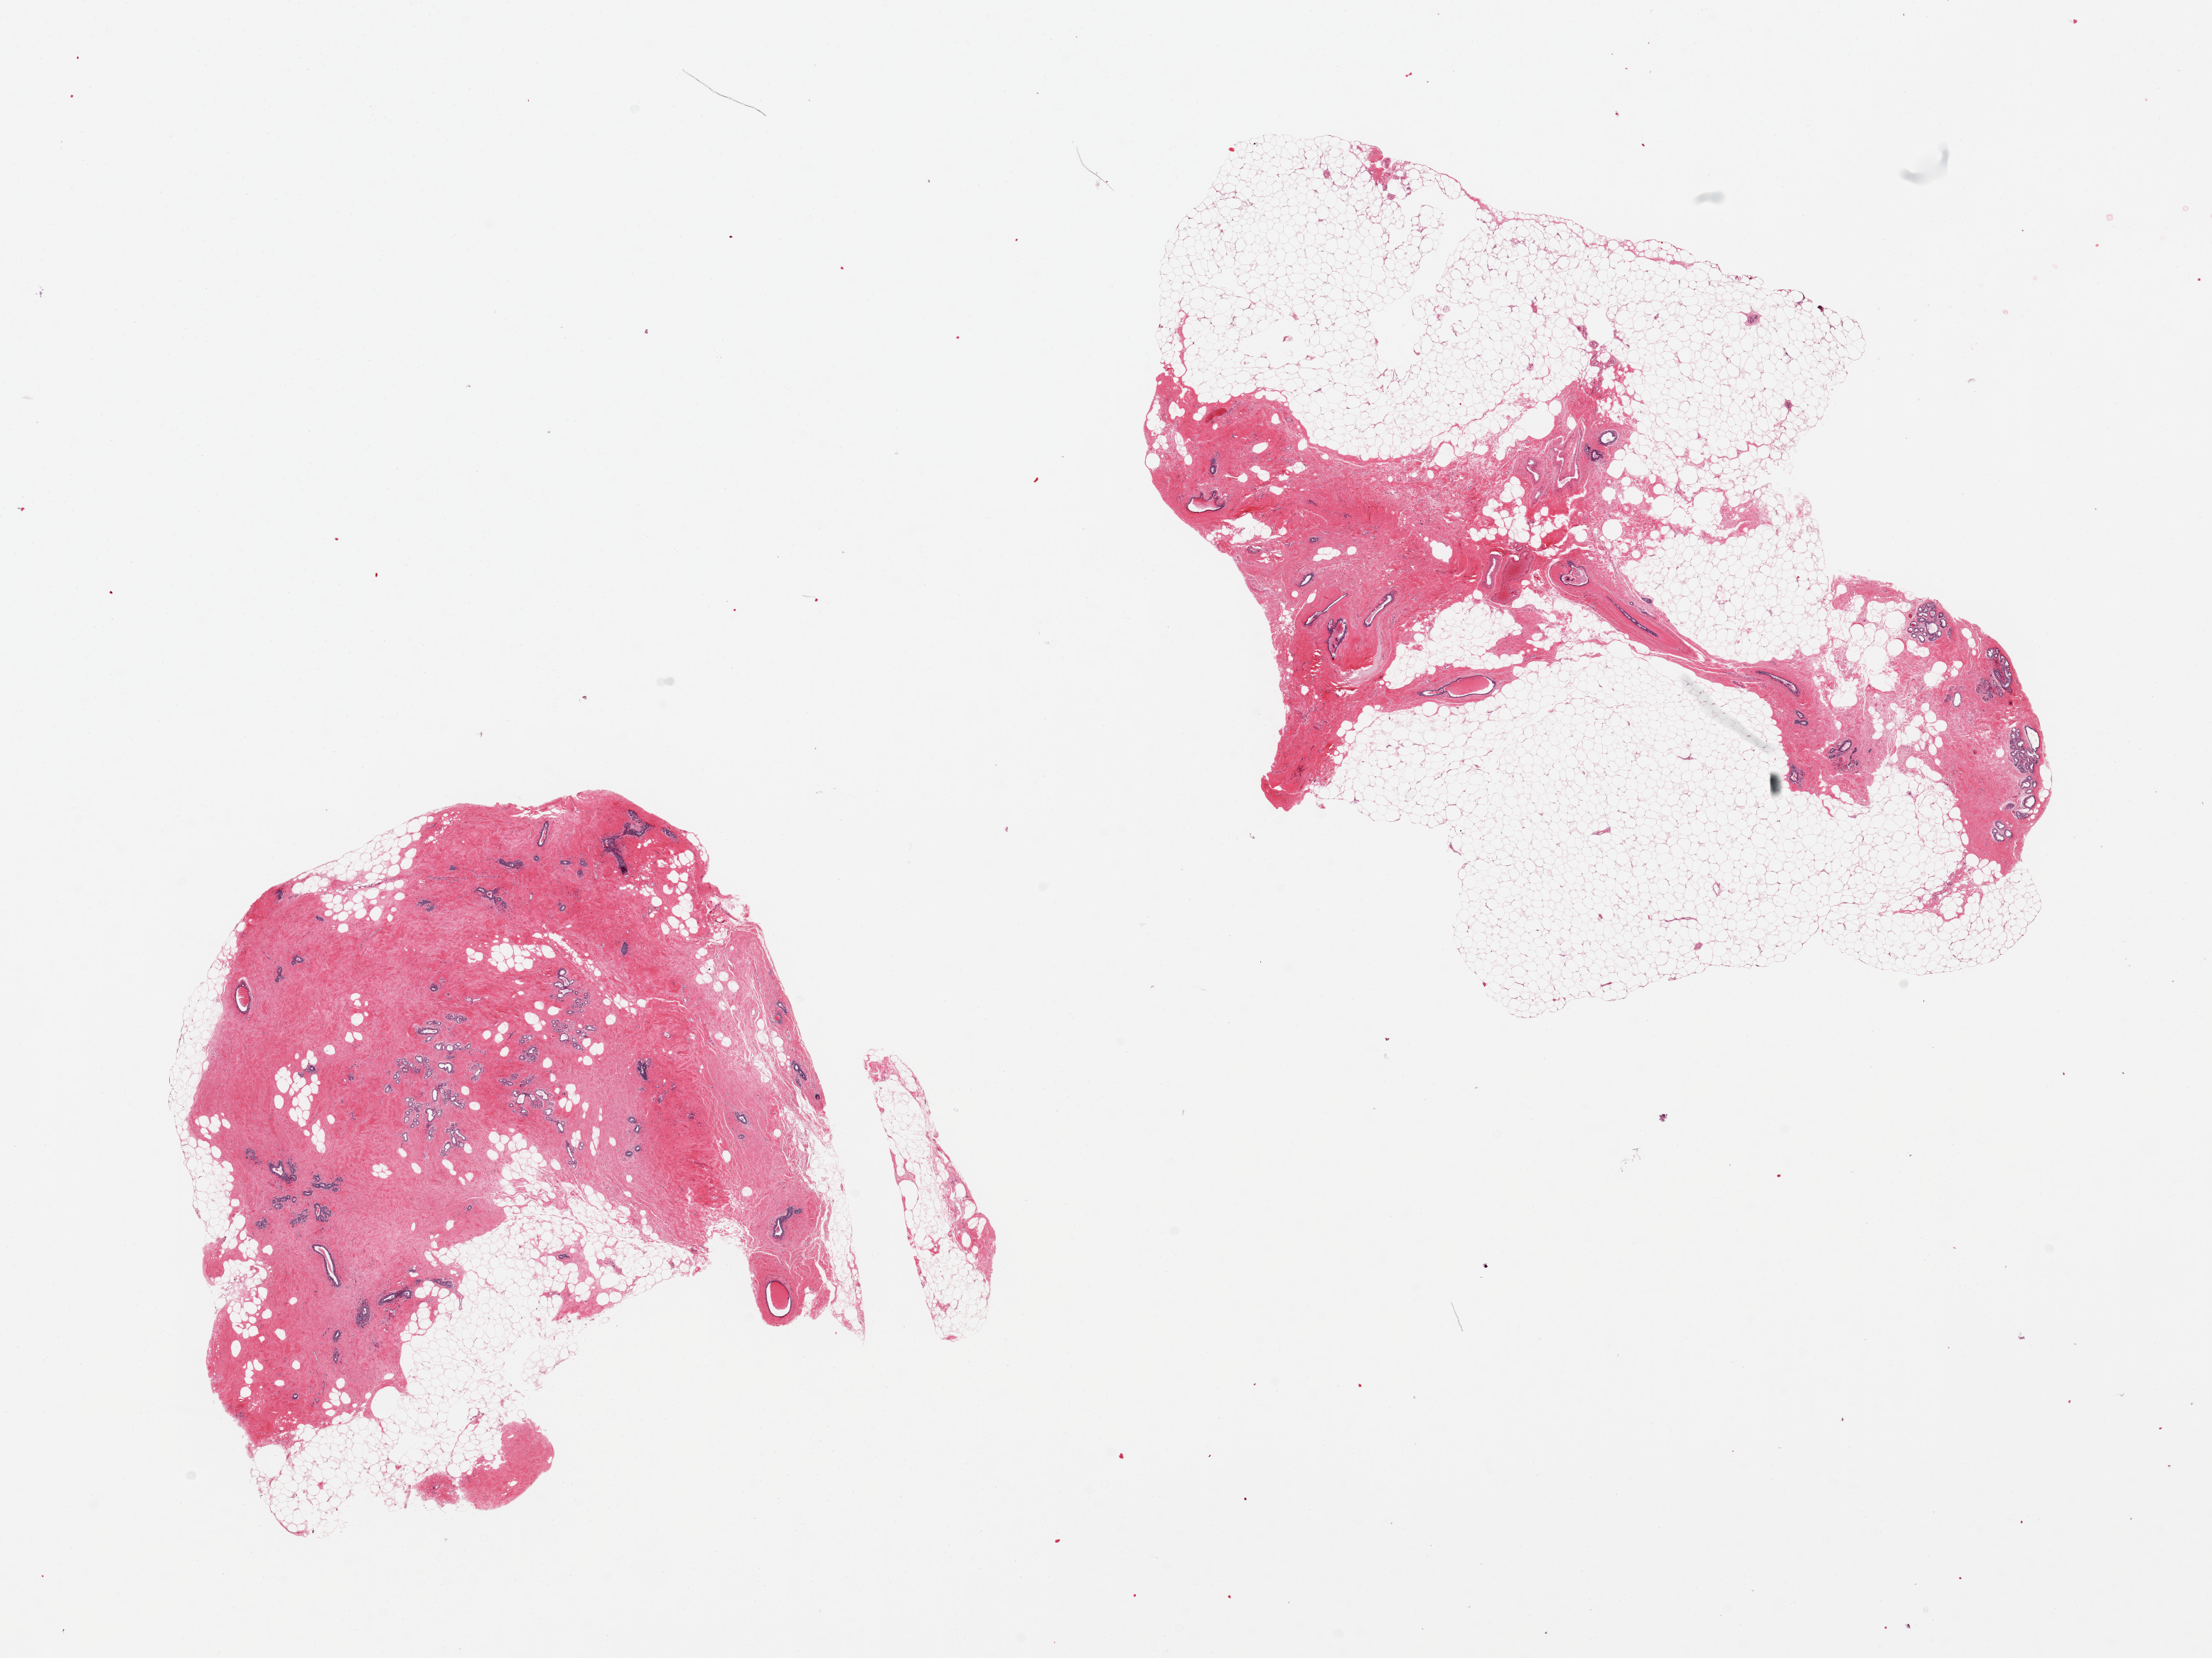
Hematoxylin and eosin (H&E) whole-slide image, whole scanned area (about 24.6 x 18.4 mm) shown as a low-resolution overview; PAXgene-fixed paraffin-embedded (PFPE) section; section of breast (target tissue); donor tissue sample. Donor: female.
Pathologist's review note for this sample: 2 pieces, foci of blunt duct adenosis.